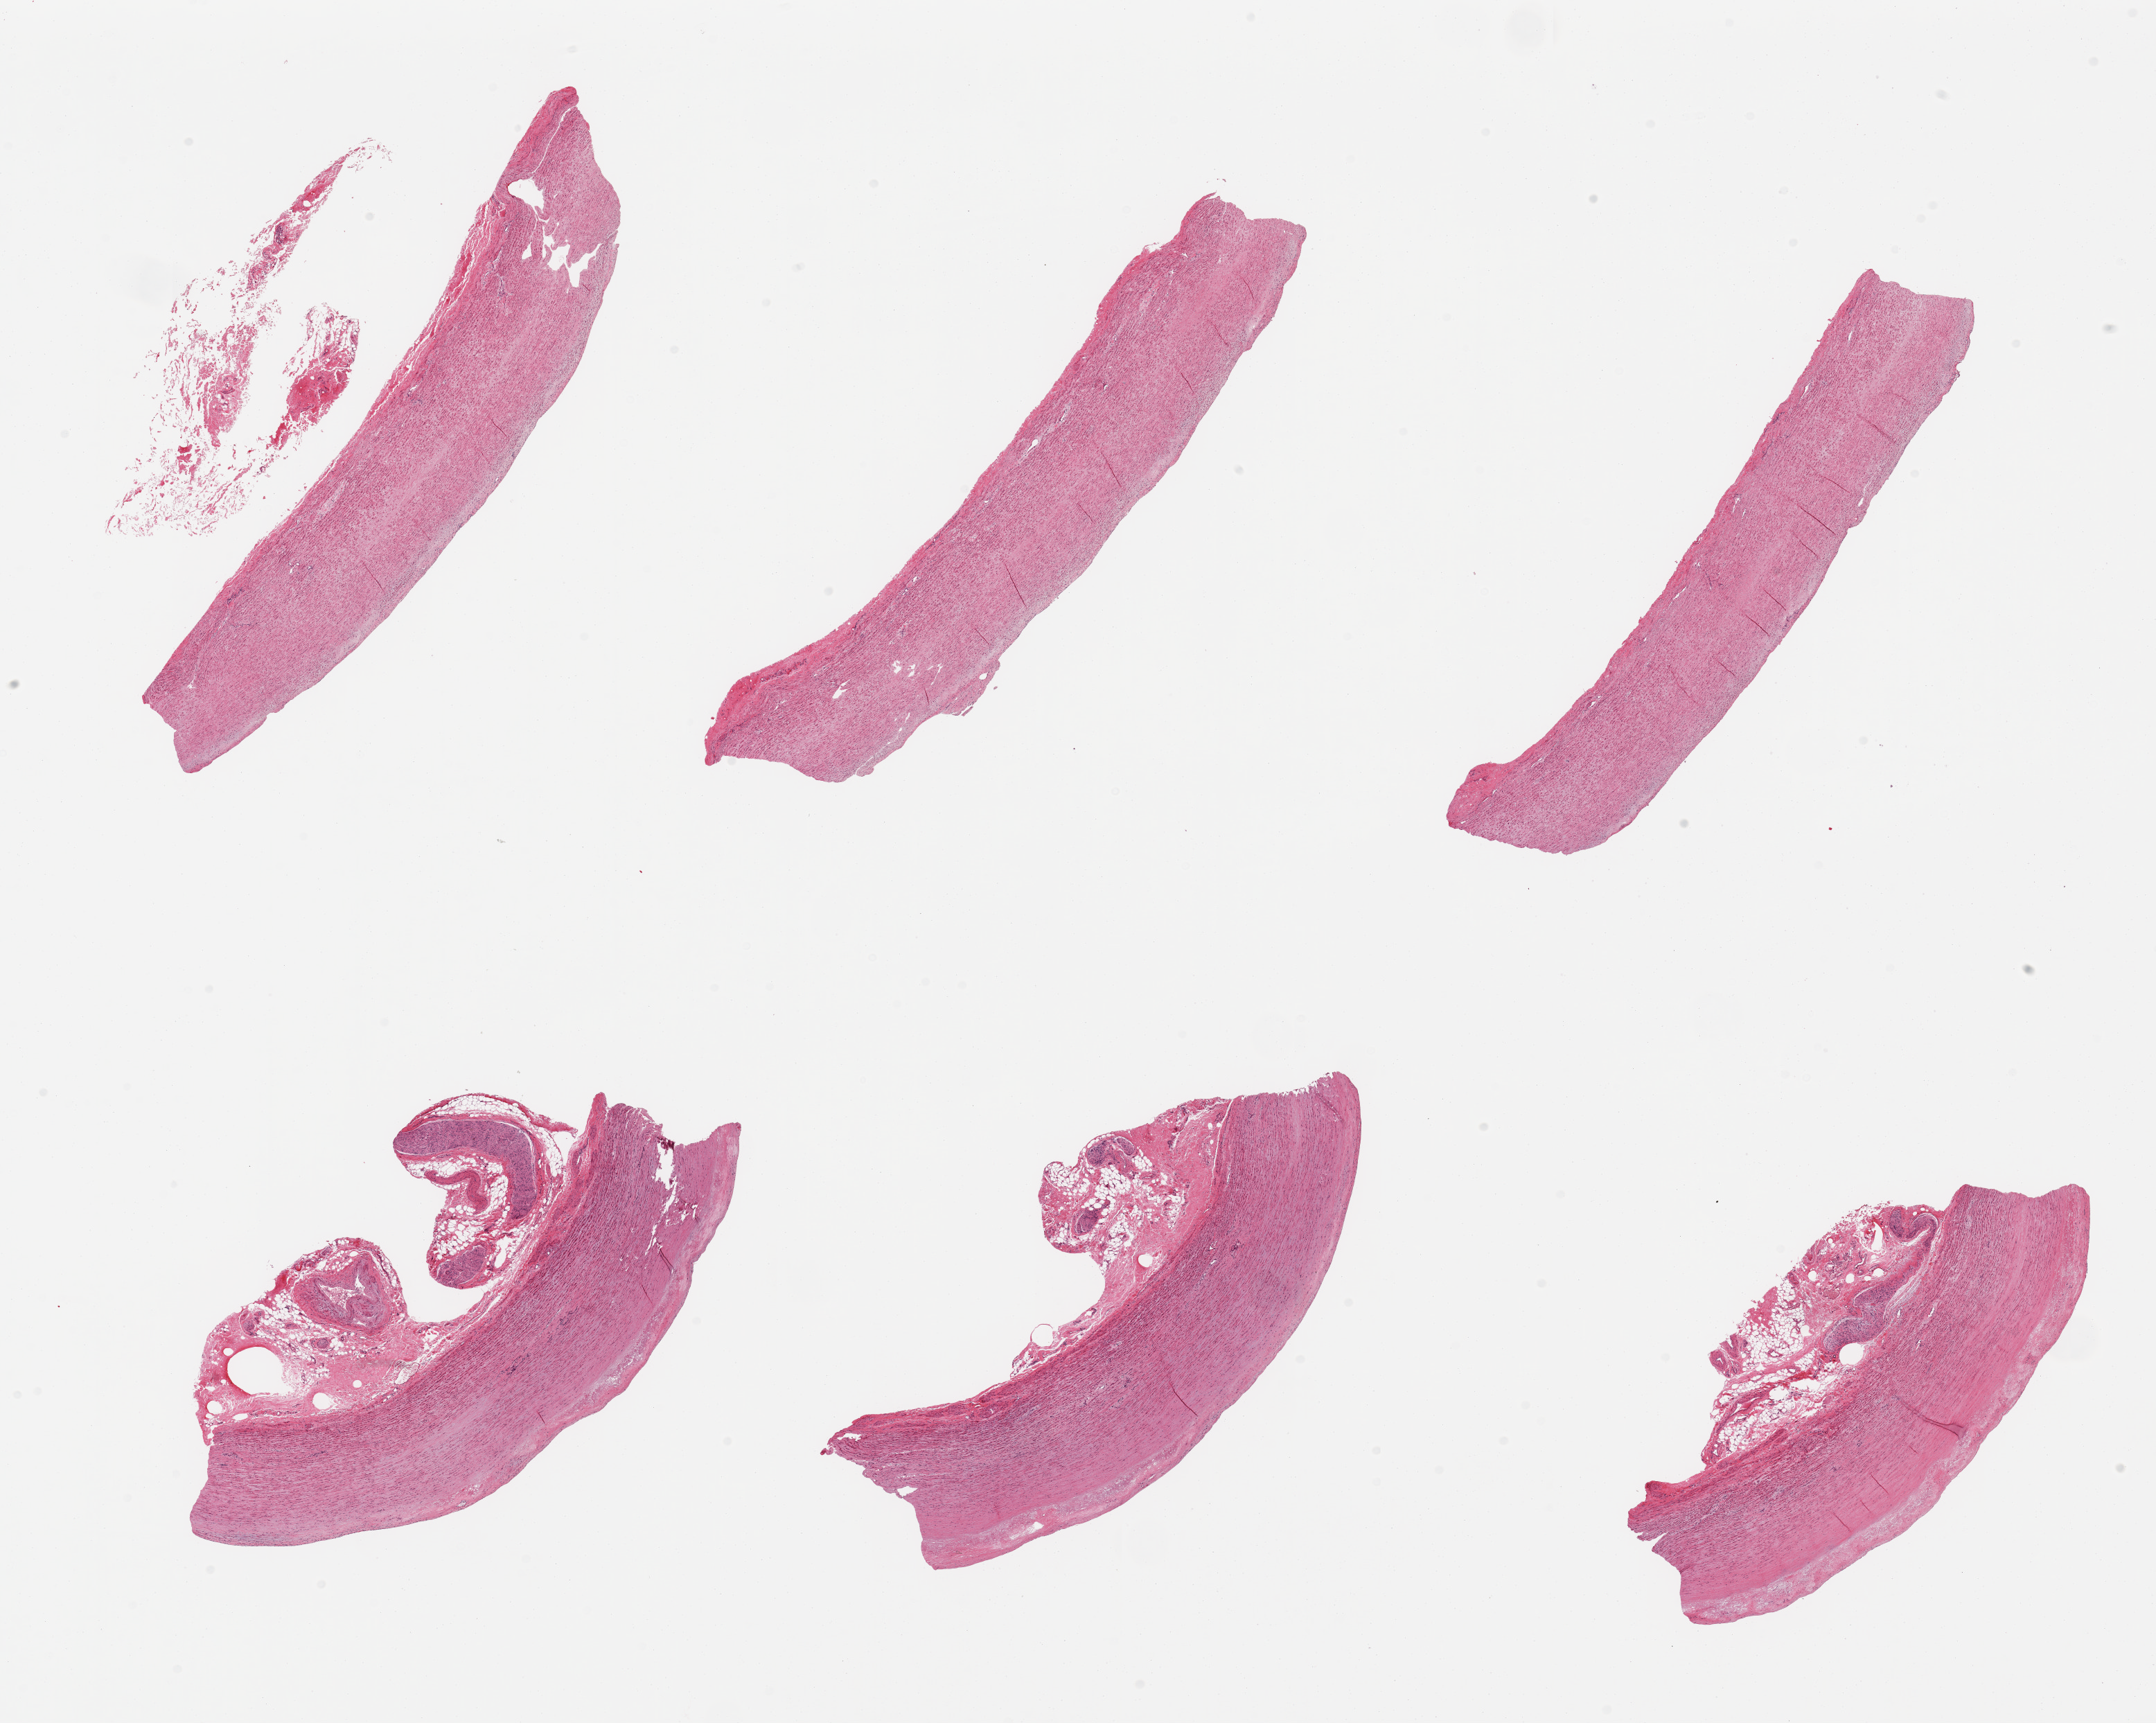
H&E whole-slide image, low-resolution overview of the scanned area, about 24.6 x 19.7 mm (from a 20x scan). PAXgene-fixed paraffin-embedded (PFPE) section. Section of aorta (target tissue). Donor tissue sample. Donor sex: male.
- reviewer comment on this tissue sample: 6 pieces; flat plaques on 3 pieces; neurofatty stroma on 3 pieces up to 1.8 mm thick